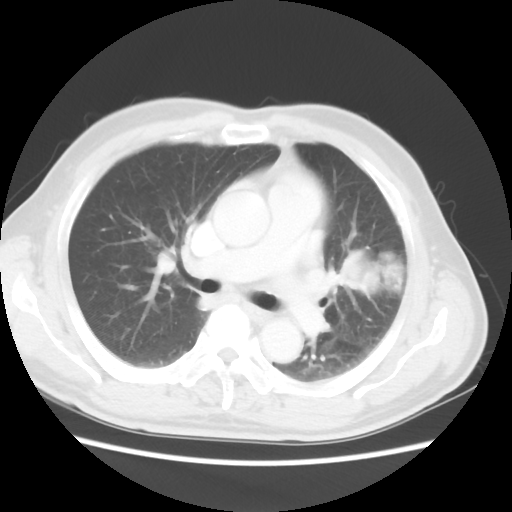
Chest CT, one axial slice; position 30 of 50 along the scan axis; reconstruction kernel STANDARD; 120 kVp; lung window (W 1500 / L -600 HU); 5 mm slice thickness; 512 × 512 image matrix, field of view 360 × 360 mm. Male patient, age 69 years. Case-level facts recorded for this patient, not image findings: clinical TNM (as recorded): T3 N1 M1a.
Structures marked on this image (rectangle marked by the reading radiologist):
- lung tumour (recorded histology: squamous cell carcinoma): box from (x=331, y=245) to (x=413, y=309) px